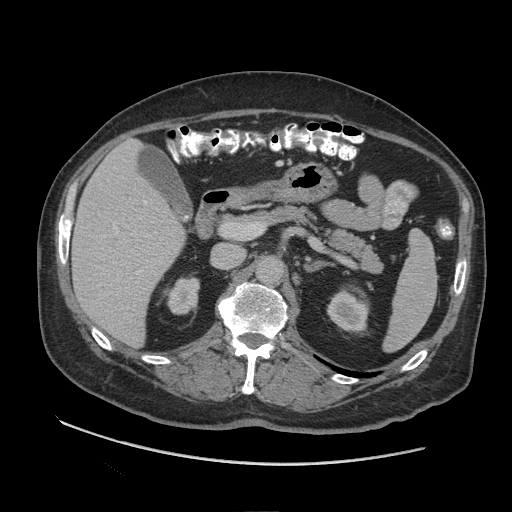
Contrast-enhanced abdominal CT (liver protocol), one axial slice. Position 49 of 109 along the scan axis. Reconstruction kernel STANDARD. Soft-tissue window (W 400 / L 40 HU). 2.5 mm slice thickness. 512 × 512 image matrix, field of view 420 × 420 mm. From the clinical record (not read from this slice): diagnosis: hepatocellular carcinoma (patient treated with transarterial chemoembolisation; whether this scan precedes or follows treatment is not stated here); TNM stage (as recorded): Stage-I; Child-Pugh class: A.
Outlined on this slice (semi-automatically segmented with operator editing):
- liver parenchyma outside the tumour (the mass and vessels are separate outlines, so this box may not span the whole liver): bounding box [x1, y1, x2, y2] px = [70, 138, 184, 346]
- liver vessels: [97, 174, 146, 274]